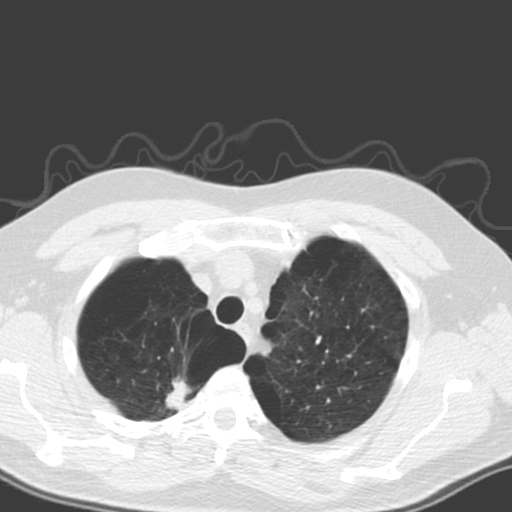
Low-dose screening chest CT, one axial slice. Lung window (W 1500 / L -600 HU). 3.2 mm slice thickness. 512 × 512 image matrix, field of view 340 × 340 mm.
Structures marked on this image (outlined manually by an expert reader):
- lesion 1 (tumor, upper lobe of right lung): bounding box [x1, y1, x2, y2] px = [165, 379, 191, 410]